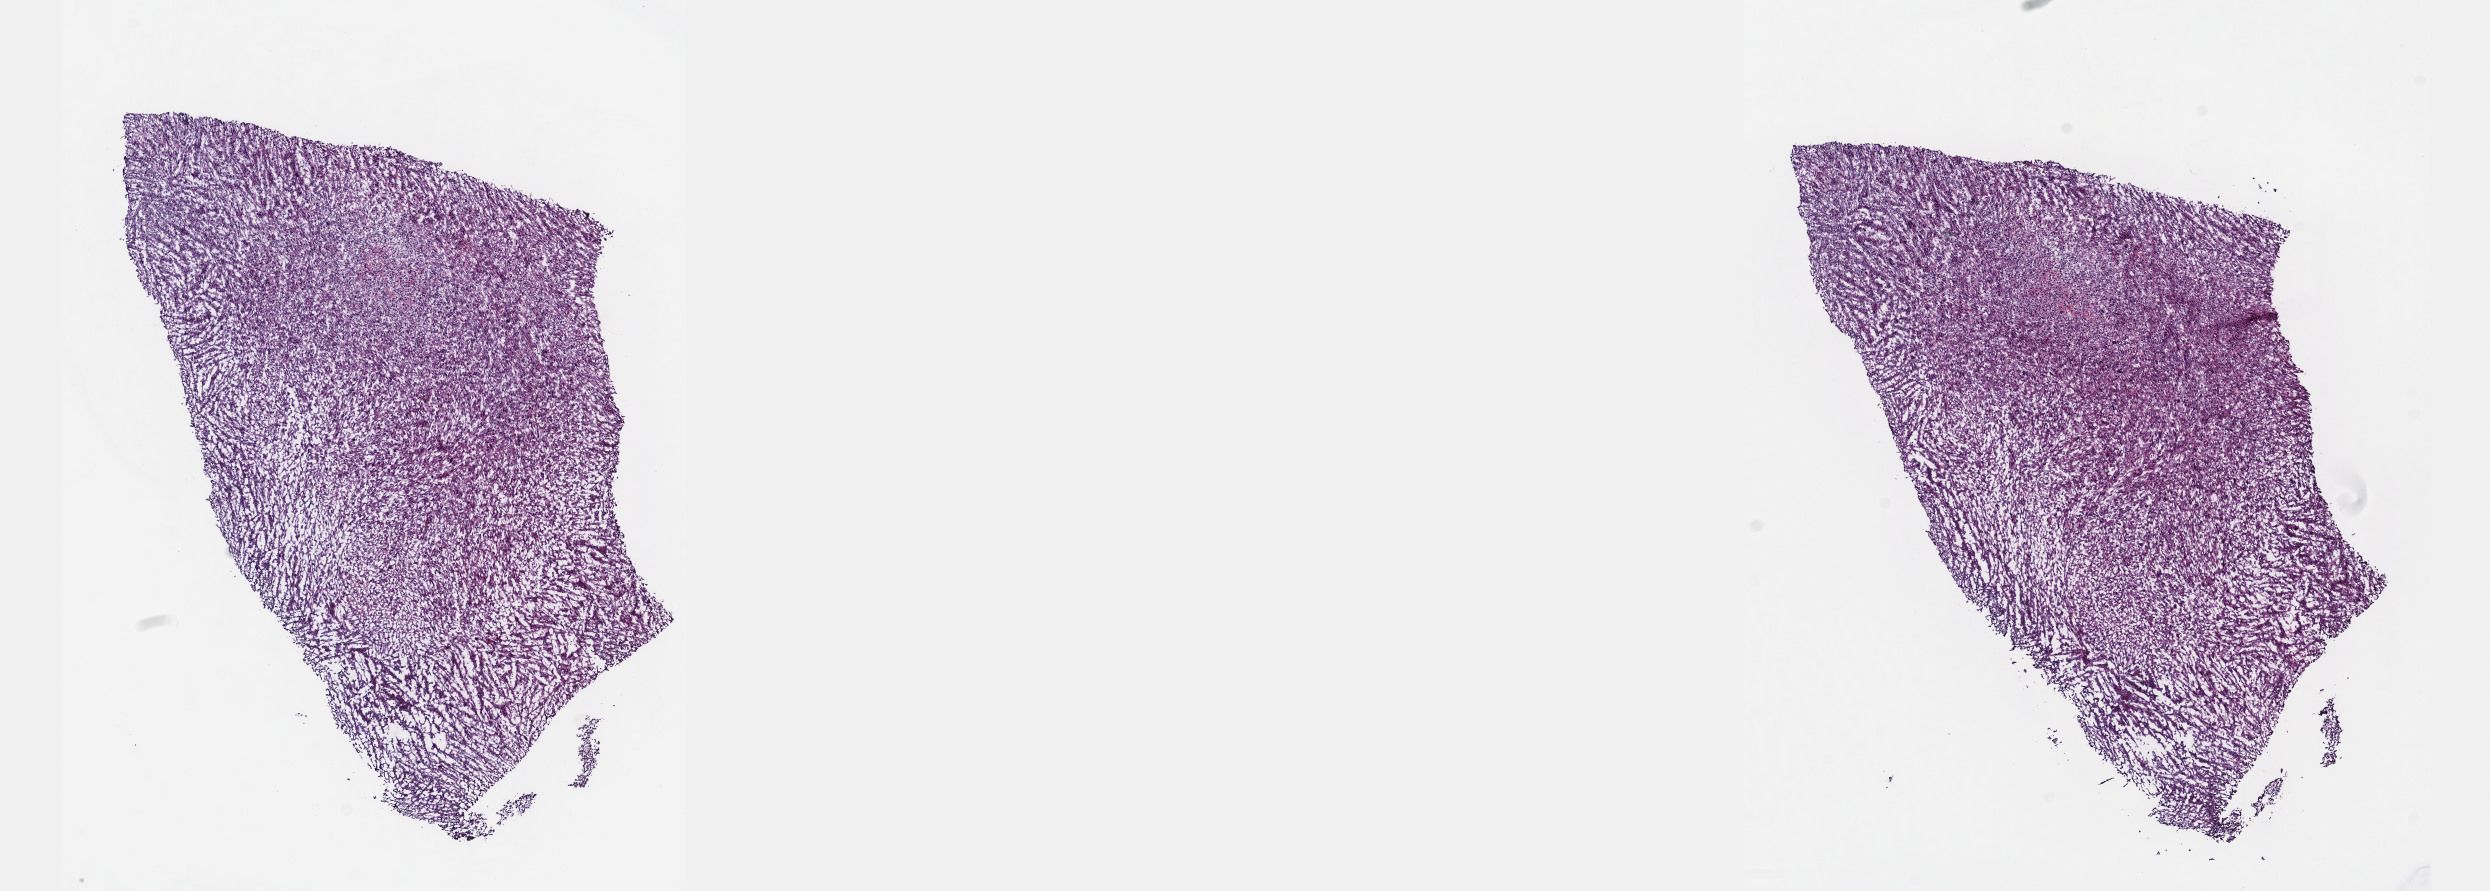
Whole-slide histology image, Hematoxylin and eosin (H&E) stained, low-resolution overview of the scanned area, about 20.1 x 7.2 mm (from a 40x scan), frozen section from the top of the tissue portion, connective, subcutaneous and other soft tissues, primary tumour sample. Female patient; age at initial diagnosis 80 years. Composition of this section per pathologist review: tumour cells 90%, tumour nuclei 100%, normal cells 0%, stromal cells 10%, necrosis 0%. Infiltration values recorded for this section: lymphocyte infiltration 0%, monocyte infiltration 0%, neutrophil infiltration 0%.
Diagnosis: Undifferentiated sarcoma (connective, subcutaneous and other soft tissues of lower limb and hip).